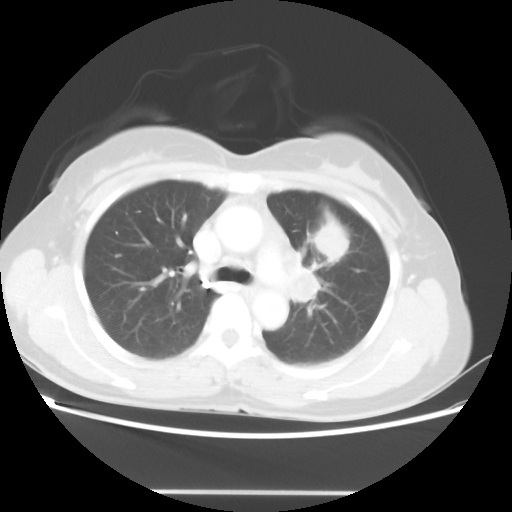
Chest CT, one axial slice. Position 31 of 46 along the scan axis. Reconstruction kernel STANDARD. 100 kVp. Lung window (W 1500 / L -600 HU). 5 mm slice thickness. 512 × 512 image matrix. Female patient, age 50 years. From the clinical record (not read from this slice): clinical TNM (as recorded): T1c N1 M0; histopathological grade: G3.
Outlined on this slice (rectangle marked by the reading radiologist):
- lung tumour (recorded histology: adenocarcinoma): box from (x=312, y=220) to (x=350, y=263) px